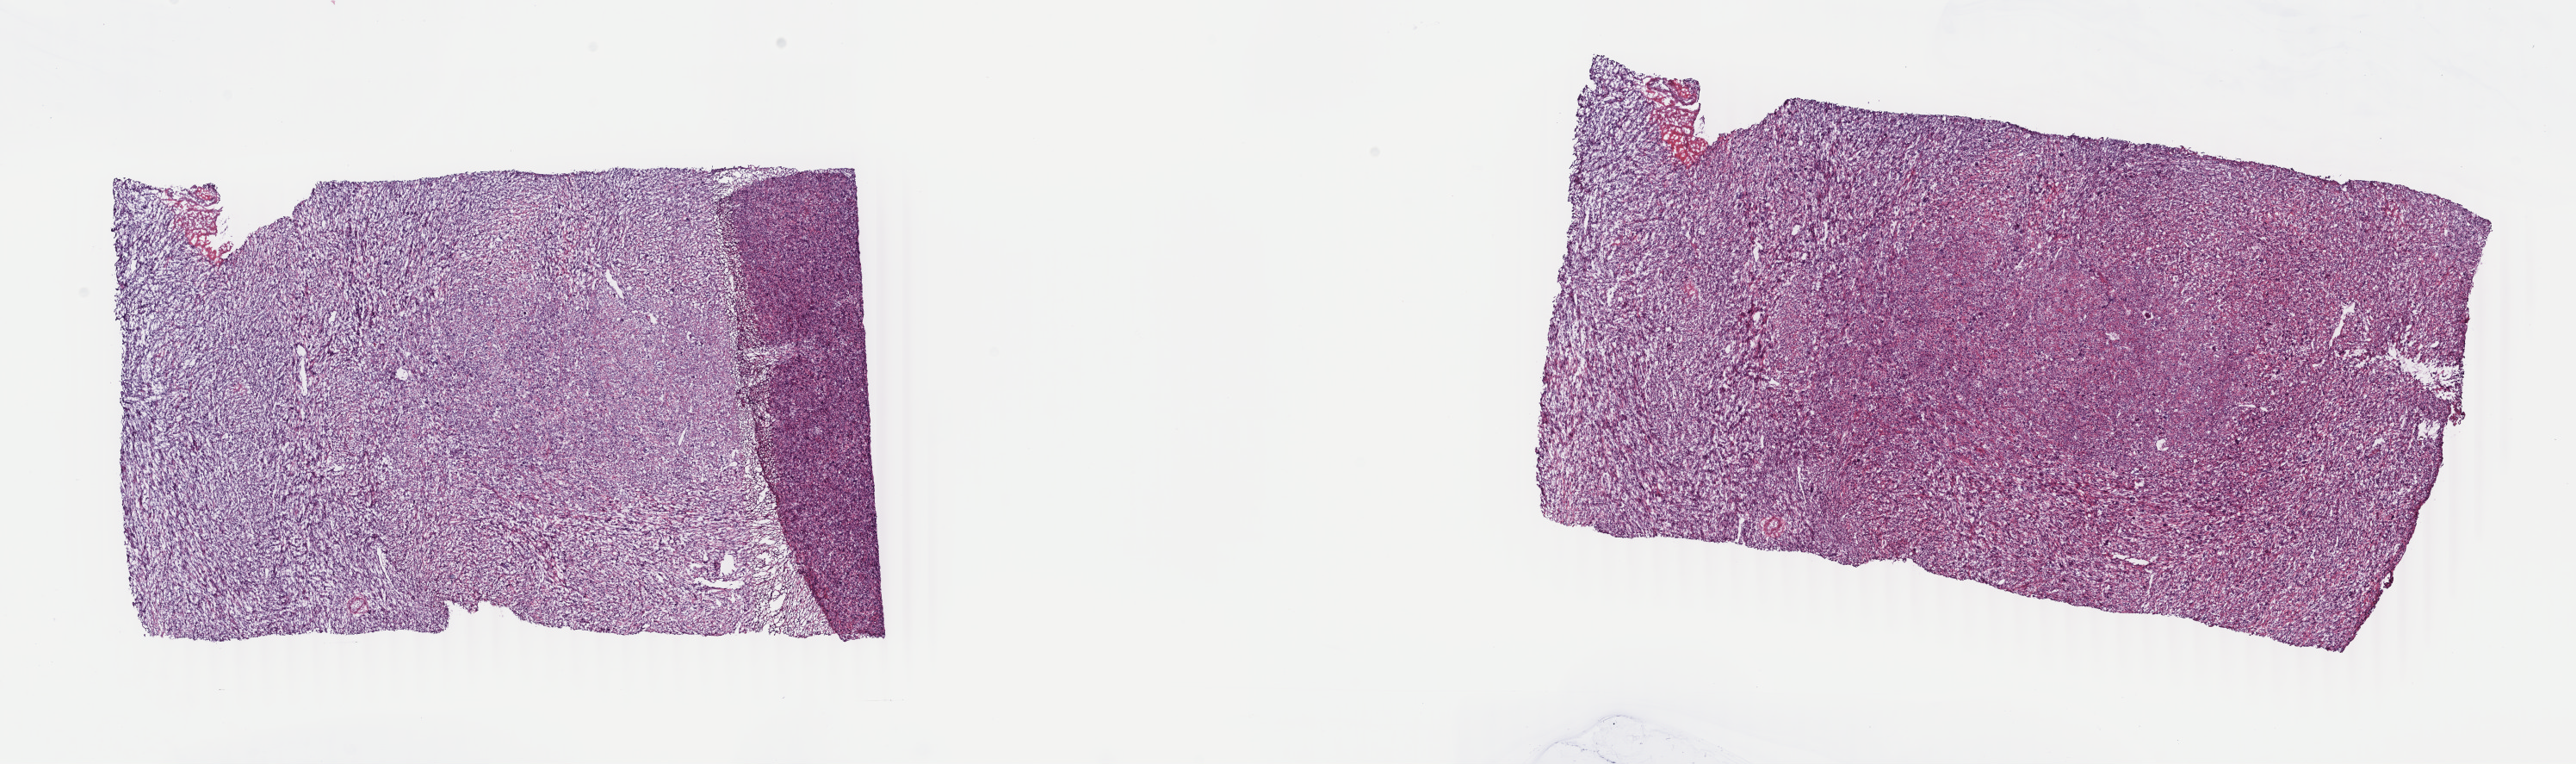
Digitized Hematoxylin and eosin (H&E) stained tissue section (whole slide) — shown as a low-resolution overview of the whole scanned area (about 23.8 x 7.1 mm); frozen section from the top of the tissue portion; primary tumour sample from the connective, subcutaneous and other soft tissues. Male, age 79 years at initial diagnosis. Pathologist review of this section (percent, as recorded): tumour cells 100%, tumour nuclei 80%, normal cells 0%, stromal cells 0%, necrosis 0%. Infiltration values recorded for this section: lymphocyte infiltration 2%, monocyte infiltration 0%, neutrophil infiltration 0%.
Pathologic diagnosis: Malignant fibrous histiocytoma (connective, subcutaneous and other soft tissues of lower limb and hip).